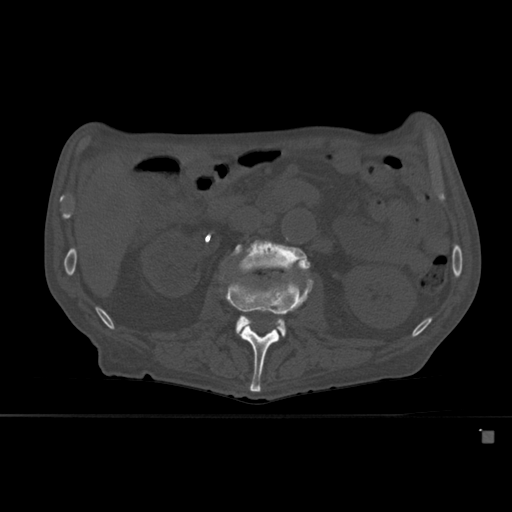
CT including the spine, one axial slice; position 228 of 527 along the scan axis; bone window (W 1800 / L 400 HU); 1.5 mm slice thickness; 512 × 512 image matrix, field of view 373 × 373 mm. Patient: male, 78 years. Case-level facts recorded for this patient, not image findings: primary cancer: prostate.
Annotated regions visible in this slice (semi-automatic segmentation, software-assisted and operator-edited):
- L2 vertebra: bounding box <225,273,314,392> (left, top, right, bottom; pixels)
- L3 vertebra: <233,237,311,336>